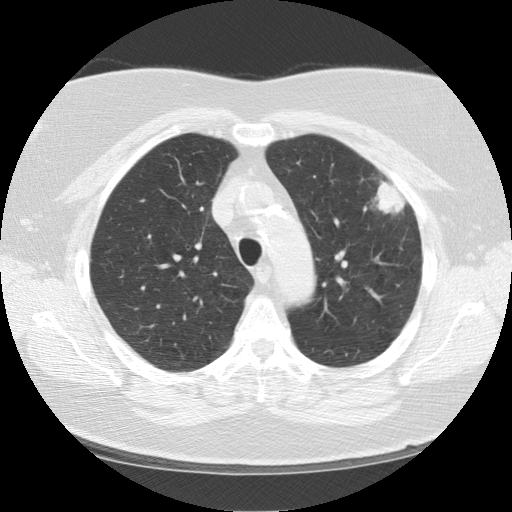
Low-dose screening chest CT, one axial slice. 120 kVp. Lung window (W 1500 / L -600 HU). 2.5 mm slice thickness. 512 × 512 image matrix, field of view 350 × 350 mm.
Outlined on this slice (expert manual segmentation):
- lesion 1 (tumor, upper lobe of left lung): bounding box <375,180,406,214> (left, top, right, bottom; pixels)